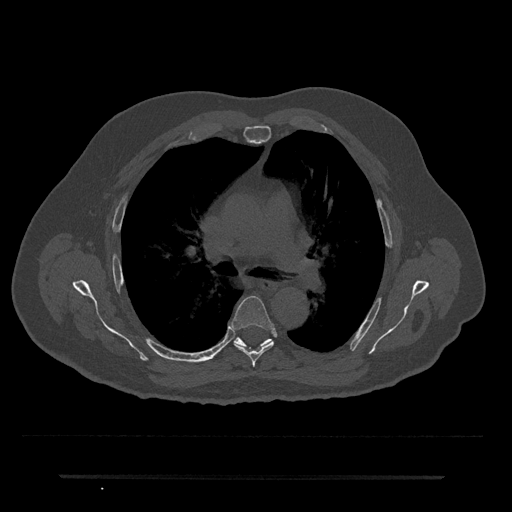
CT including the spine, one axial slice; position 468 of 797 along the scan axis; 120 kVp; bone window (W 1800 / L 400 HU); 512 × 512 image matrix. Patient: male, 69 years. Case-level facts recorded for this patient, not image findings: primary cancer: prostate.
Structures marked on this image (semi-automatic segmentation, software-assisted and operator-edited):
- T5 vertebra: bounding box <230,296,274,367> (left, top, right, bottom; pixels)
- T6 vertebra: <235,337,270,346>